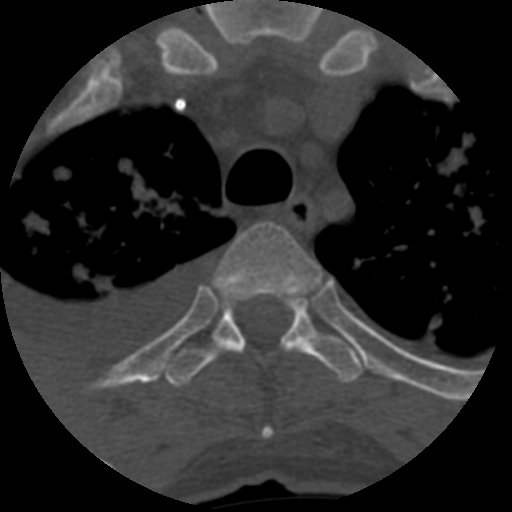
CT including the spine, one axial slice; position 479 of 708 along the scan axis; 120 kVp; one of 3 acquisitions stored at this slice position; bone window (W 1800 / L 400 HU); 1.25 mm slice thickness; 512 × 512 image matrix. Patient age 55 years. From the clinical record (not read from this slice): primary cancer: colon.
Outlined on this slice (semi-automatic segmentation, software-assisted and operator-edited):
- T3 vertebra: bounding box <218,222,322,438> (left, top, right, bottom; pixels)
- T4 vertebra: <164,286,365,388>